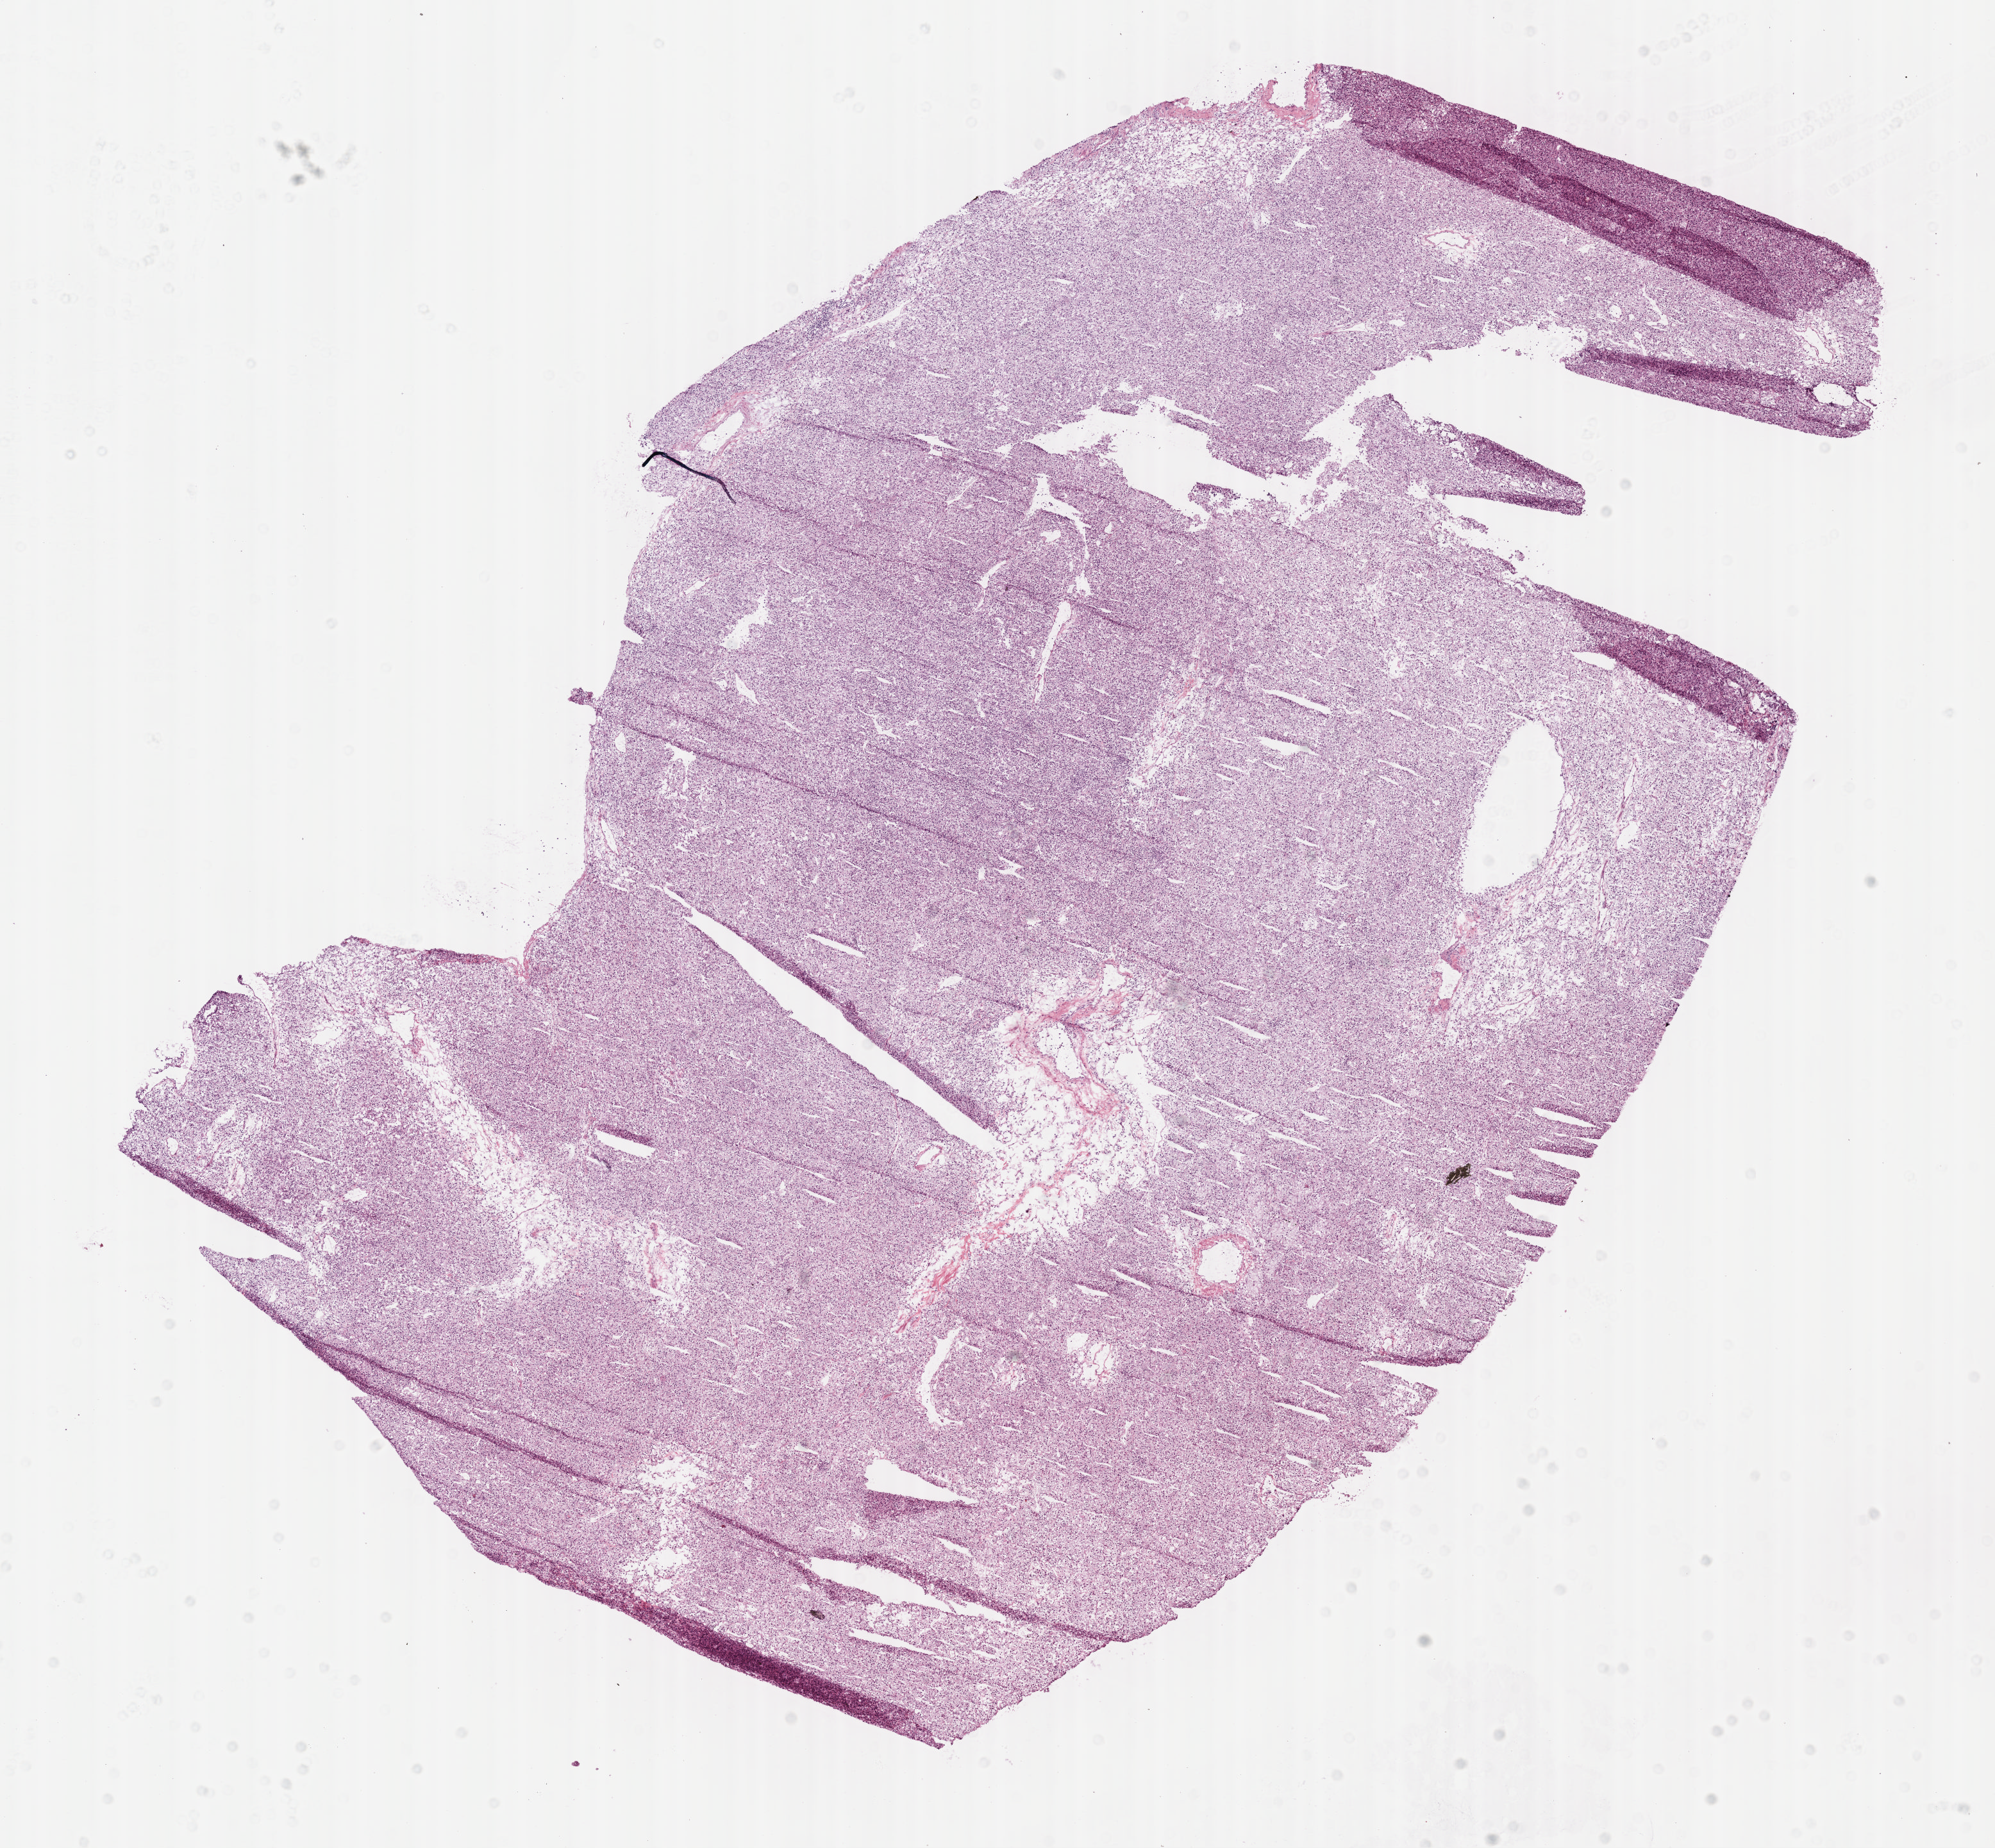
Whole-slide histology image, Hematoxylin and eosin (H&E) stained — a low-resolution overview of the entire scanned area, about 12.6 x 11.7 mm (acquisition: 40x scan), frozen section from the bottom of the tissue portion, primary tumour sample from the kidney. Male patient; age at initial diagnosis 74 years.
Histologic diagnosis: Clear cell adenocarcinoma, NOS.